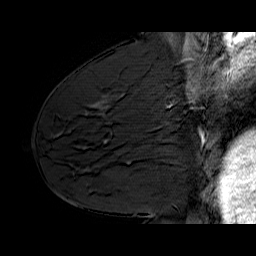
Breast MRI (dynamic contrast-enhanced), one sagittal slice; slice 32 of 60 in the series (ordered by position); dynamic contrast-enhanced series, time point 2 of 6 at this slice position (early post-contrast); 1.5 T; TE 6.4 ms, TR 32.9 ms; 256 × 256 image matrix, field of view 200 × 200 mm. Female patient. Case-level facts recorded for this patient, not image findings: setting: breast cancer imaged before/during neoadjuvant chemotherapy; receptor status: HER2-positive.
Structures marked on this image (semi-automatically segmented with operator editing):
- analysis volume of interest (the breast-tissue region the enhancement analysis was run in; not a lesion): box from (x=136, y=62) to (x=210, y=128) px
- tumour enhancement mask (voxels above the 100 % enhancement threshold inside the analysis volume of interest): (x=187, y=80)–(x=193, y=91)